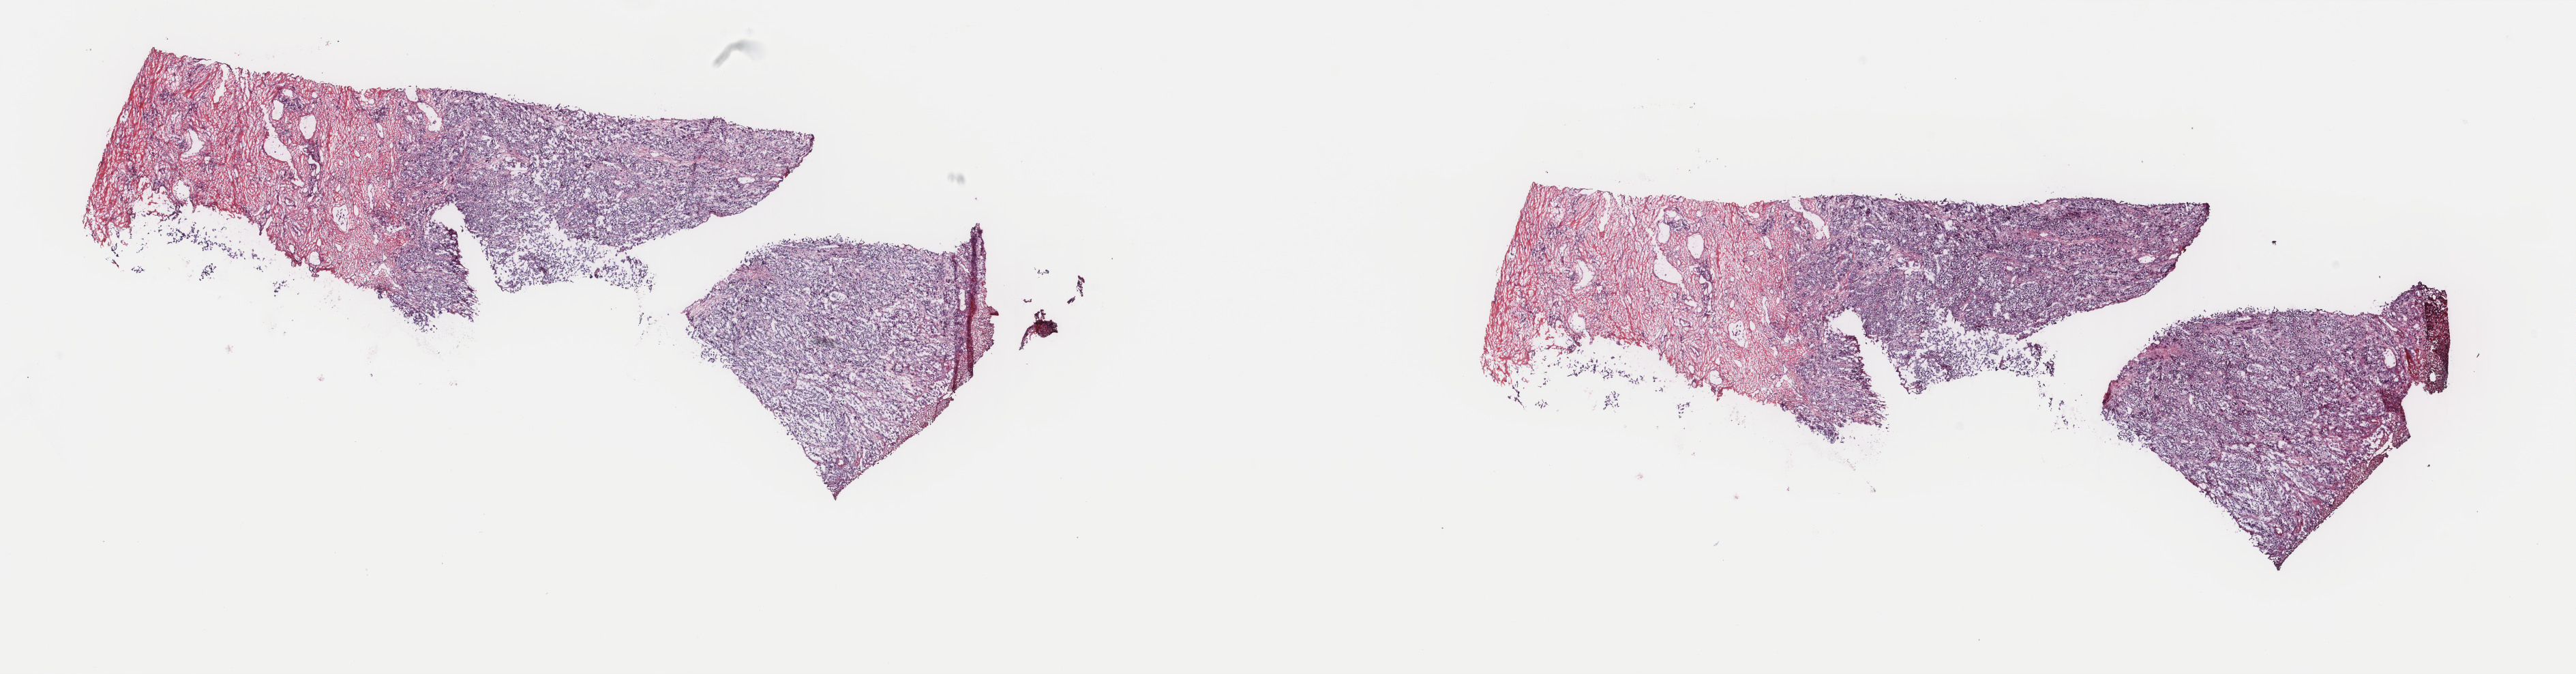
Digitized H&E-stained tissue section (whole slide), low-resolution overview of the scanned area, about 30.0 x 7.8 mm (from a 40x scan), frozen section, primary tumour sample from the skin. Male patient; age at initial diagnosis 49 years. Composition of this section per pathologist review: tumour cells 70%, tumour nuclei 80%, normal cells 29%, stromal cells 0%, necrosis 1%. Infiltration values recorded for this section: lymphocyte infiltration 2%, monocyte infiltration 0%, neutrophil infiltration 0%.
AJCC pathologic stage: IIIC (7th edition). Diagnosis: Malignant melanoma, NOS.